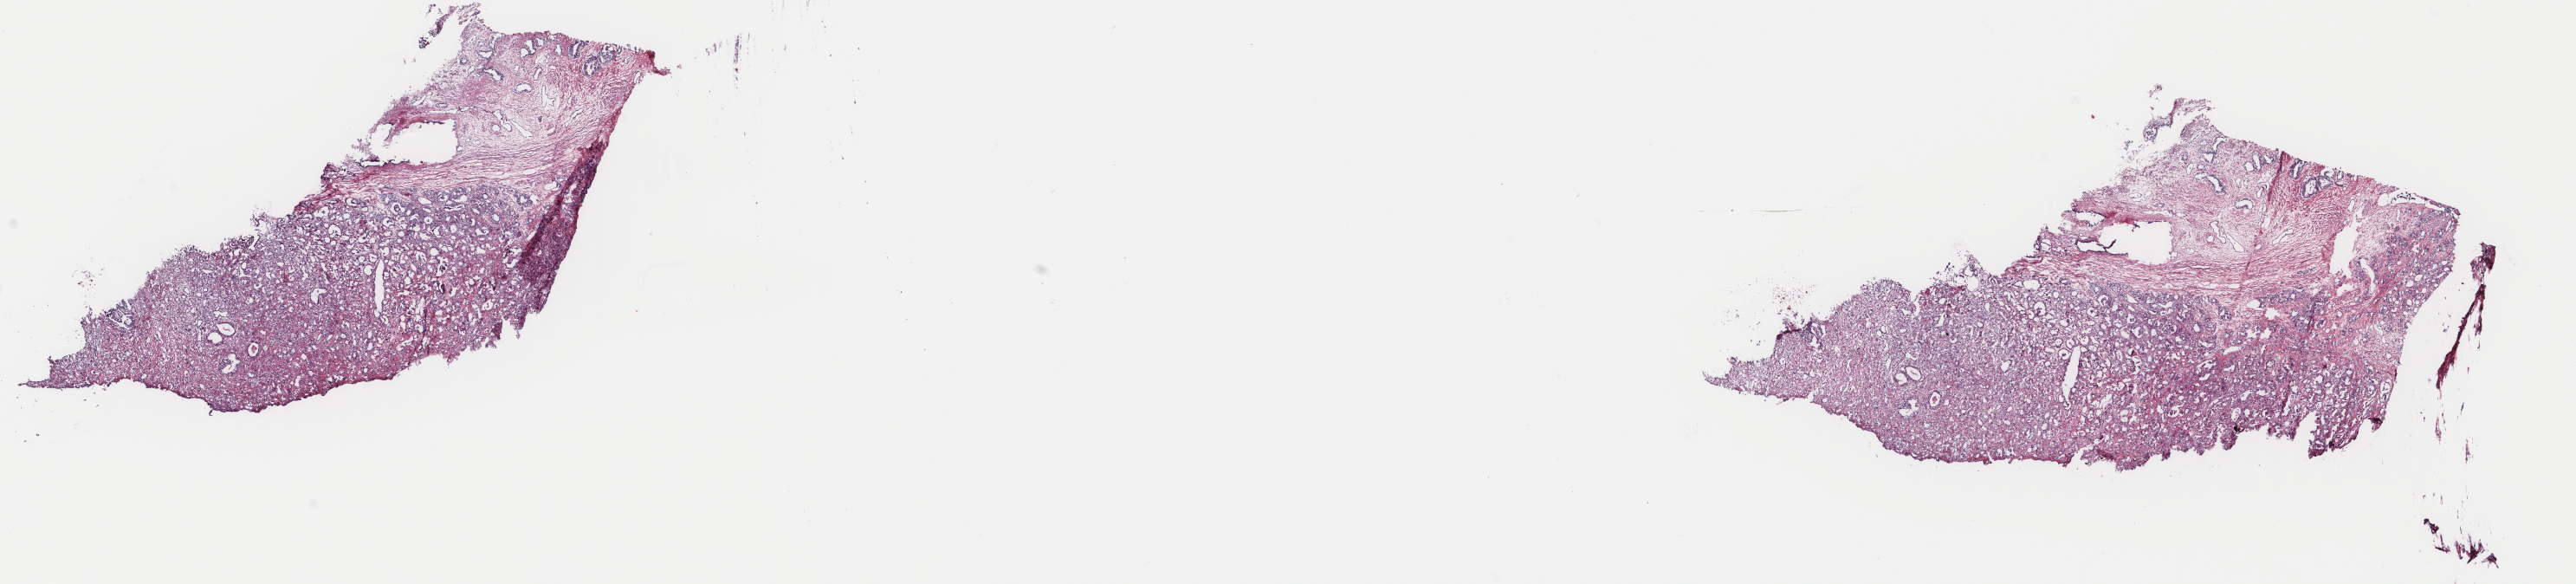
Whole-slide histology image, H&E — whole scanned area (about 23.6 x 5.4 mm, slide scanned at 40x) shown as a low-resolution overview; frozen section from the top of the tissue portion; primary tumour sample from the prostate. Male, age 69 years at initial diagnosis. Gleason score: 9 (4+5). Pathologist review of this section (percent, as recorded): tumour cells 40%, tumour nuclei 80%, normal cells 2%, stromal cells 57%, necrosis 1%. Infiltration values recorded for this section: lymphocyte infiltration 2%, monocyte infiltration 0%, neutrophil infiltration 0%.
Lymph nodes positive (case pathology): 0 of 5 examined. Histologic diagnosis: Adenocarcinoma, NOS (prostate gland).